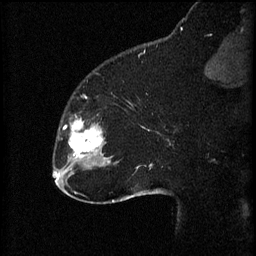
Breast MRI (dynamic contrast-enhanced), one sagittal slice; 3 images stored at this slice position (order not interpretable as contrast timing); 1.5 T; TE 4.2 ms, TR 8.2 ms; 256 × 256 image matrix, field of view 180 × 180 mm. Patient: female, 32 years.
Structures marked on this image (semi-automatically segmented with operator editing):
- analysis volume of interest (the breast-tissue region the enhancement analysis was run in; not a lesion): bounding box (x1, y1, x2, y2) in pixels: (58, 114, 111, 165)
- tumour enhancement mask (voxels above the 70 % enhancement threshold inside the analysis volume of interest): (70, 122, 103, 159)